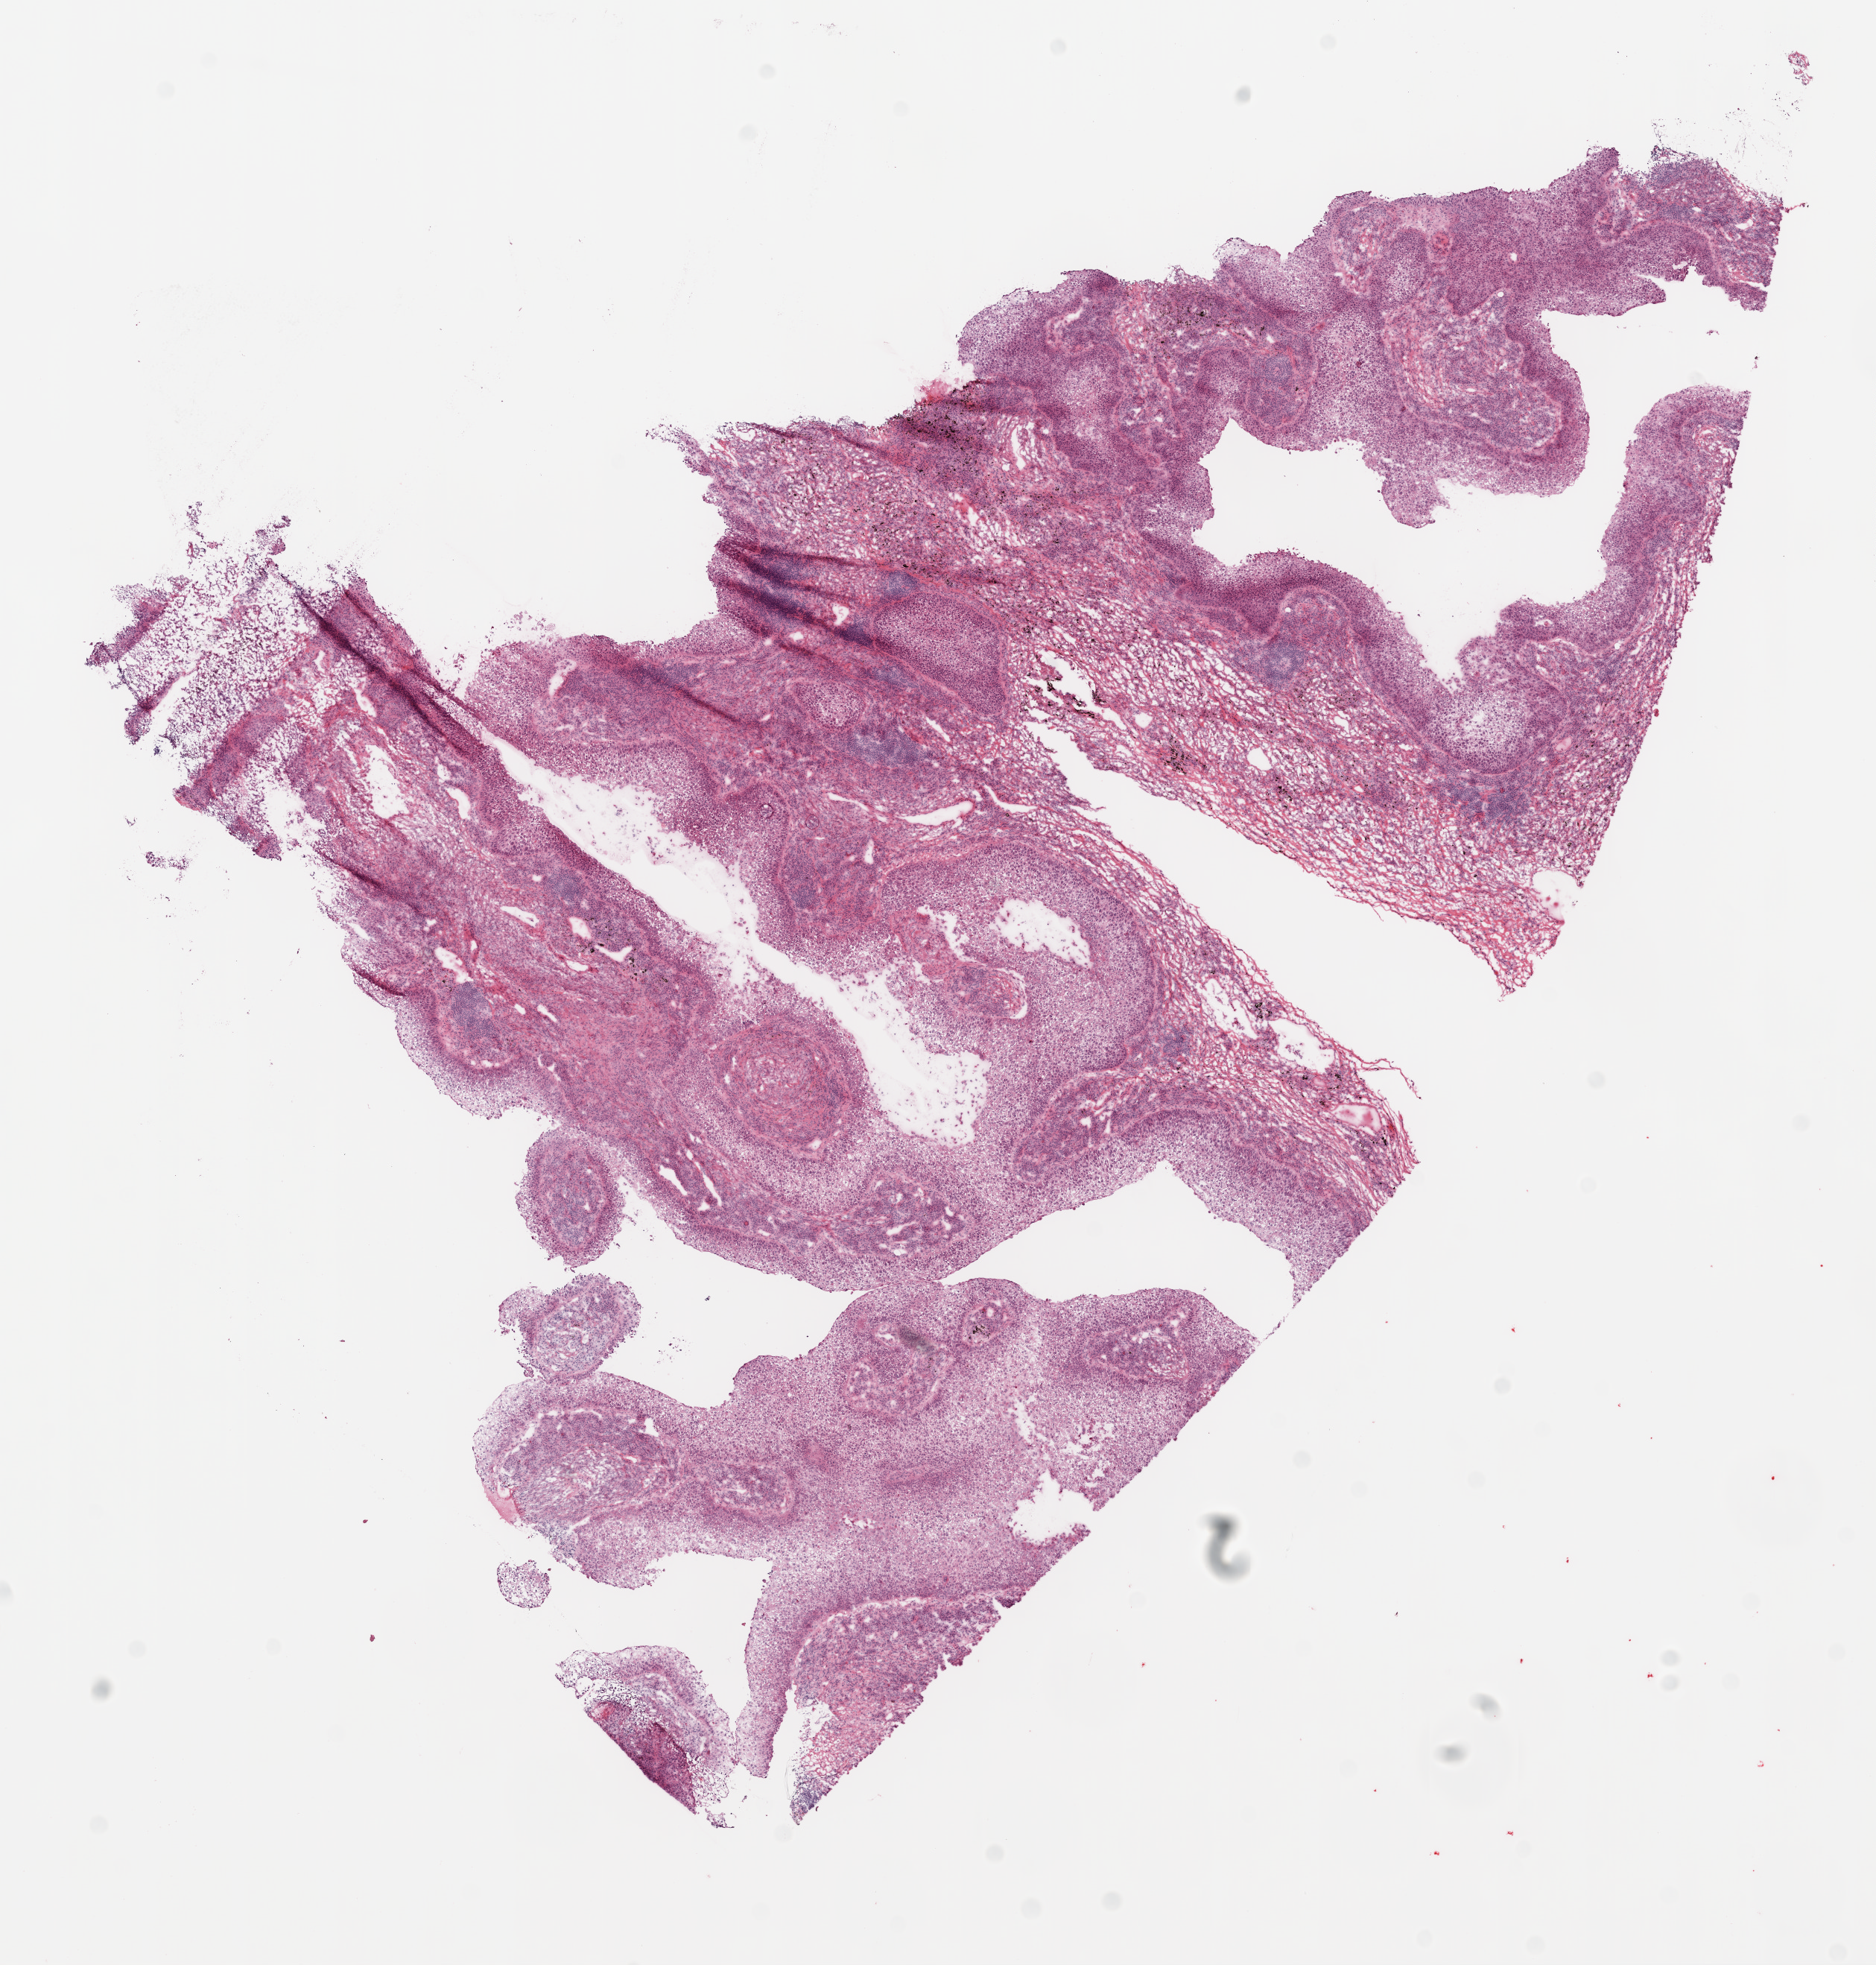
H&E-stained whole-slide image — low-resolution overview of the scanned area, about 10.2 x 10.6 mm, frozen section, sample: primary tumour, lung. Male, age 73 years at initial diagnosis. Composition of this section per pathologist review: tumour nuclei 60%, necrosis 5%.
Laterality: right. AJCC pathologic stage: IB. Pathologic diagnosis: Squamous cell carcinoma, NOS. TNM: T2 N0 M0.